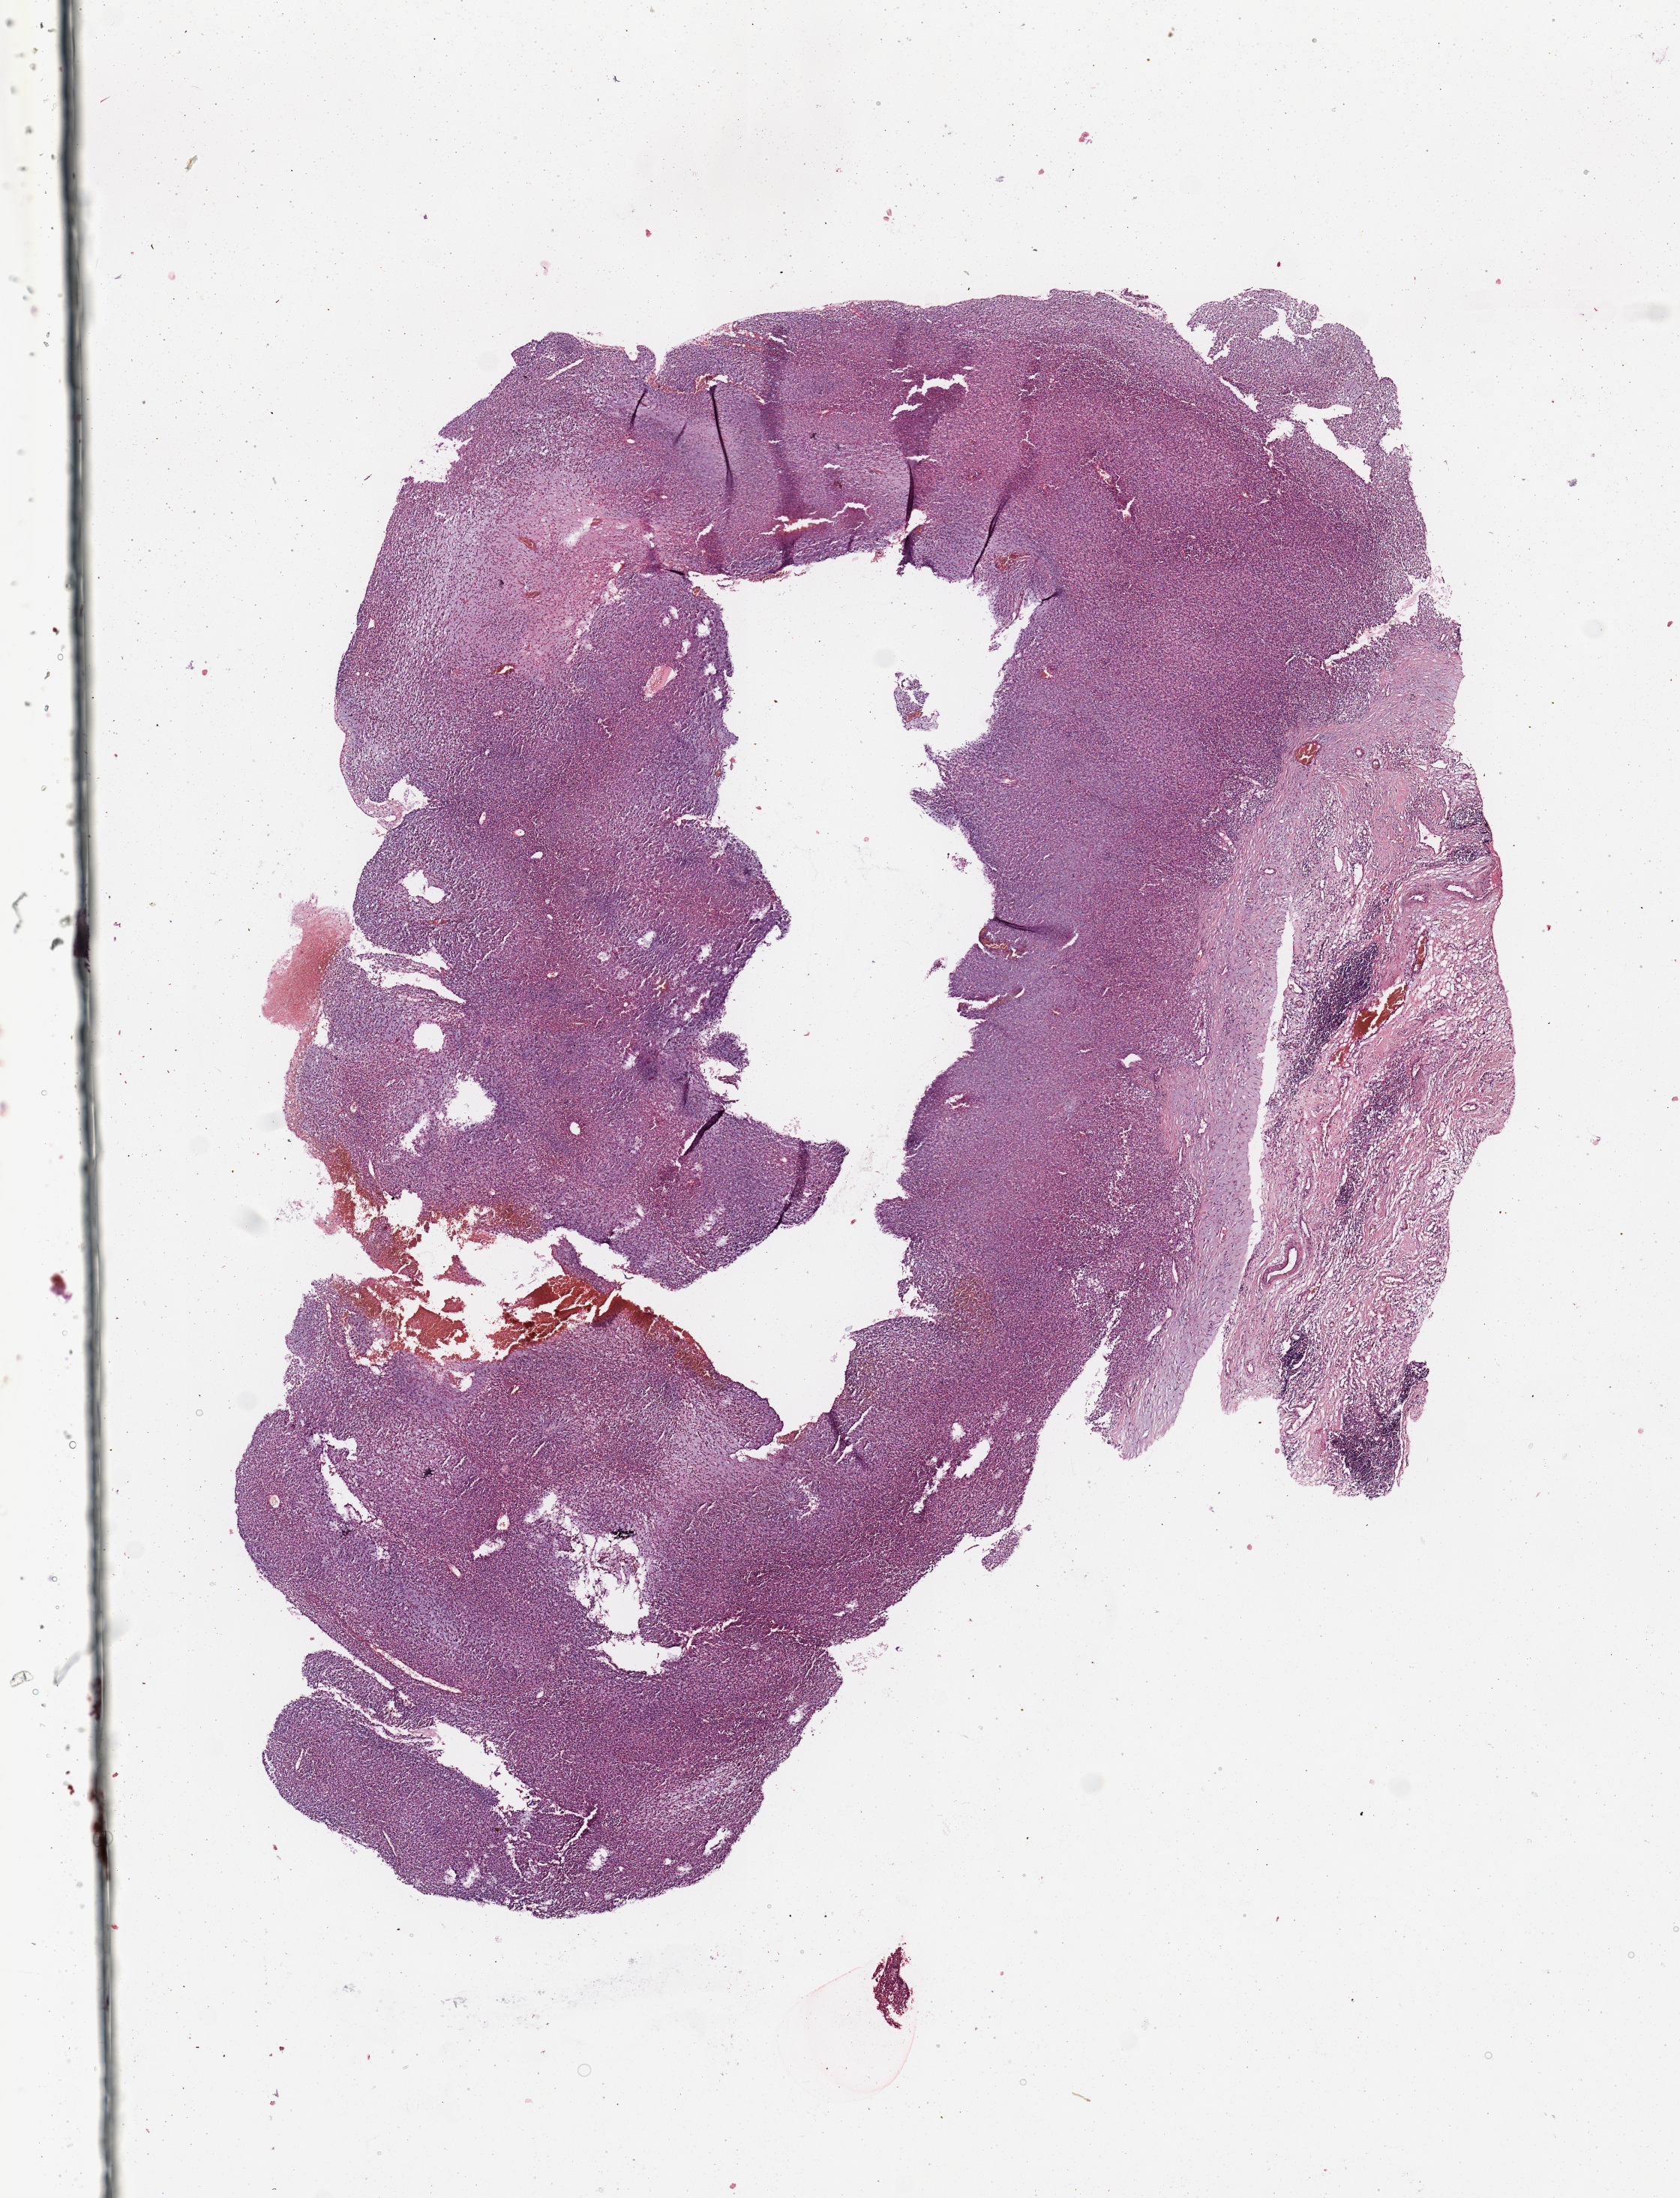
Whole-slide histology image, H&E-stained — shown as a low-resolution overview of the whole scanned area (about 8.9 x 11.6 mm, slide scanned at 20x), tumour tissue sample, sampled site: lymph node. Patient: female, age 68 years. Pathologist review of this section (percent, as recorded): tumour nuclei 90%, necrosis 0%.
* this section: metastatic tumour tissue
* patient diagnosis: Malignant melanoma, NOS
* primary tumour site (as recorded): extremities